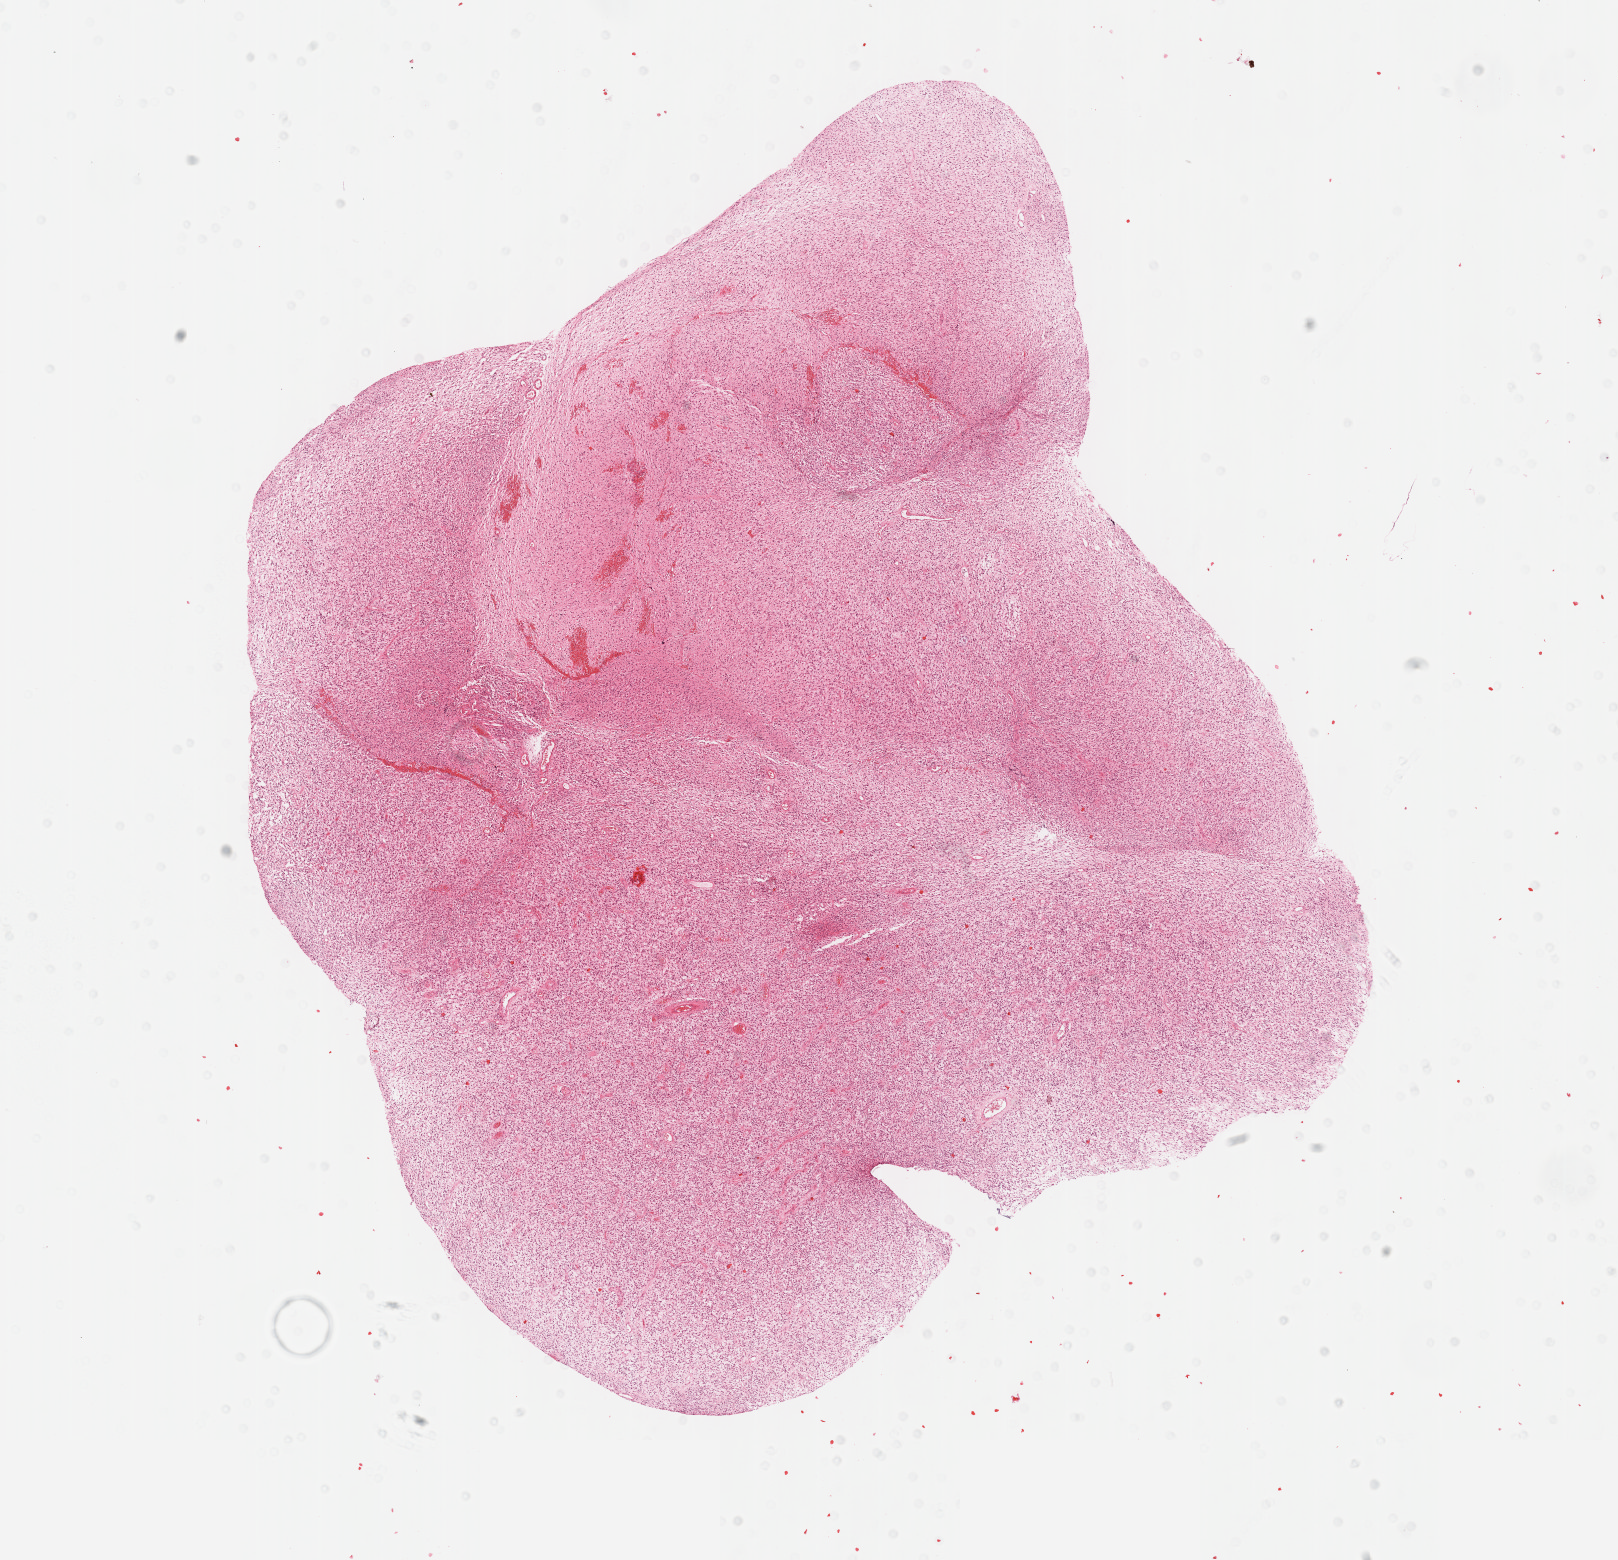
Whole-slide histology image, H&E, a low-resolution overview of the entire scanned area, about 13.1 x 12.6 mm (from a 40x scan); FFPE section; brain, primary tumour sample. Patient: male, age at initial diagnosis 50 years. Histologic grade: G3 (poorly differentiated).
Laterality: right. Diagnosis: Mixed glioma (cerebrum).